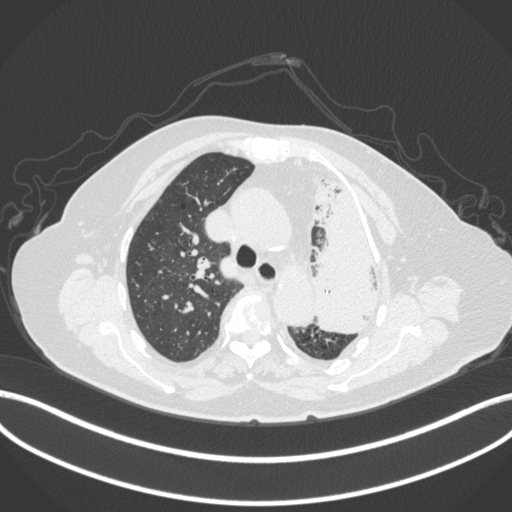
Chest CT, one axial slice. Slice 283 of 399 in the series (ordered by position). 120 kVp. Lung window (W 1500 / L -600 HU). 1 mm slice thickness. 512 × 512 image matrix, field of view 400 × 400 mm. Female patient, age 75 years. From the clinical record (not read from this slice): clinical TNM (as recorded): T3 N3 M1.
Outlined on this slice (bounding box drawn by a radiologist):
- lung tumour (recorded histology: adenocarcinoma): bounding box <310,171,393,334> (left, top, right, bottom; pixels)